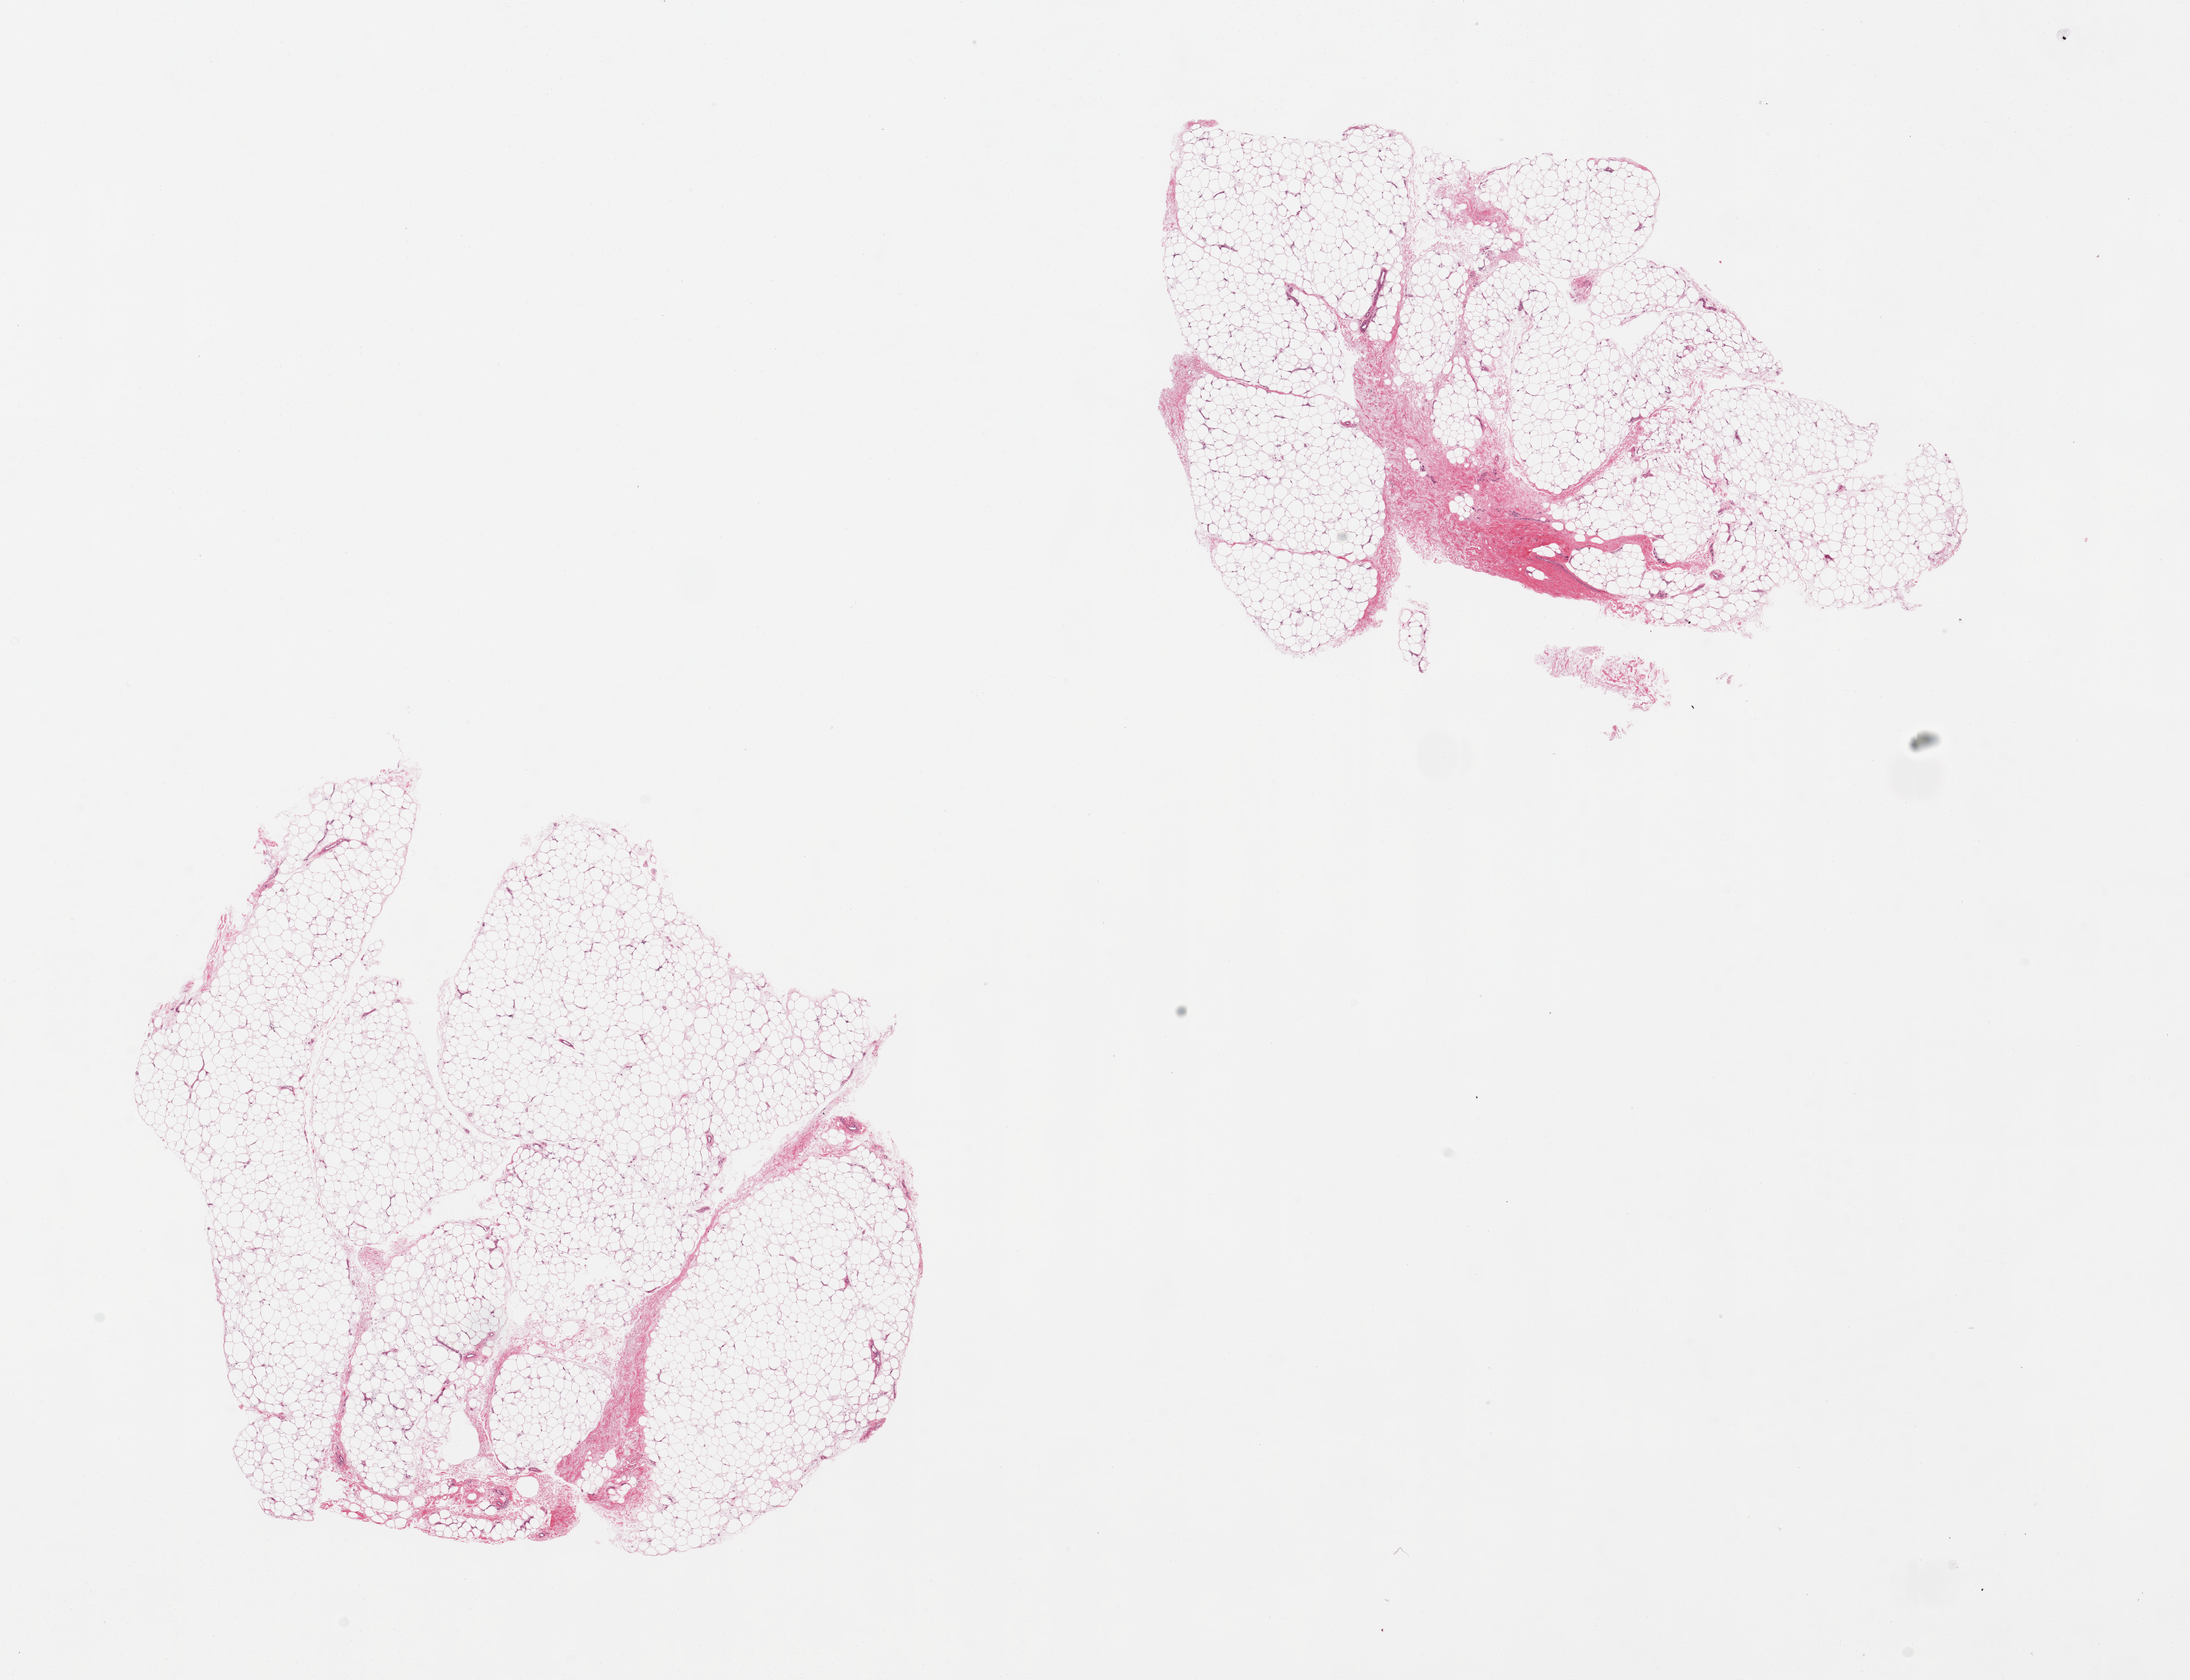
Whole-slide image, haematoxylin and eosin stain — low-resolution overview of the scanned area, about 23.6 x 18.1 mm; PAXgene-fixed, paraffin-embedded tissue; target tissue: adipose tissue; tissue donor sample. Female donor.
Reviewer comment on this tissue sample: 2 pieces. 9x8 & 9.5x6mm. well fixed; 10% stroma in one.